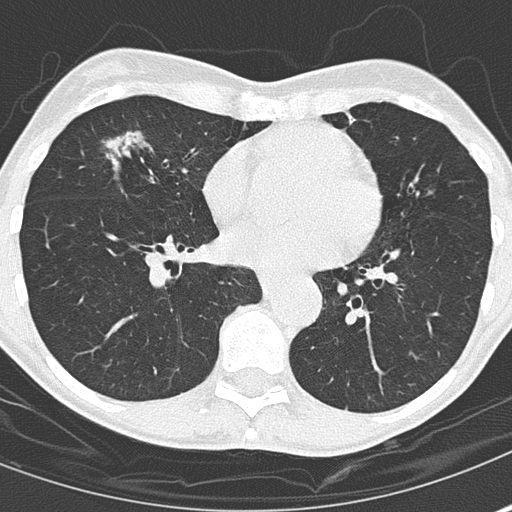
Axial slice from a low-dose chest CT screening exam. Second screening round (one year after baseline). Lung window (W 1500 / L -600 HU). 2 mm slice thickness. Lung (sharp) reconstruction kernel (B50f). Slice 101 of 167 in the series. Female, age 67 years at enrolment. Current smoker at enrolment.
Expert-annotated lung lesion, bounding box <83,116,185,206> (left, top, right, bottom; pixels). The screening reader recorded 2 non-calcified nodules or masses ≥4 mm on this exam (right middle lobe, right middle lobe); which of them this box marks is not recorded. Later outcome: lung cancer diagnosed 475 days after this screen — bronchiolo-alveolar adenocarcinoma, NOS, right middle lobe, well differentiated (G1), stage IA (AJCC 6th edition), 25 mm at pathology.